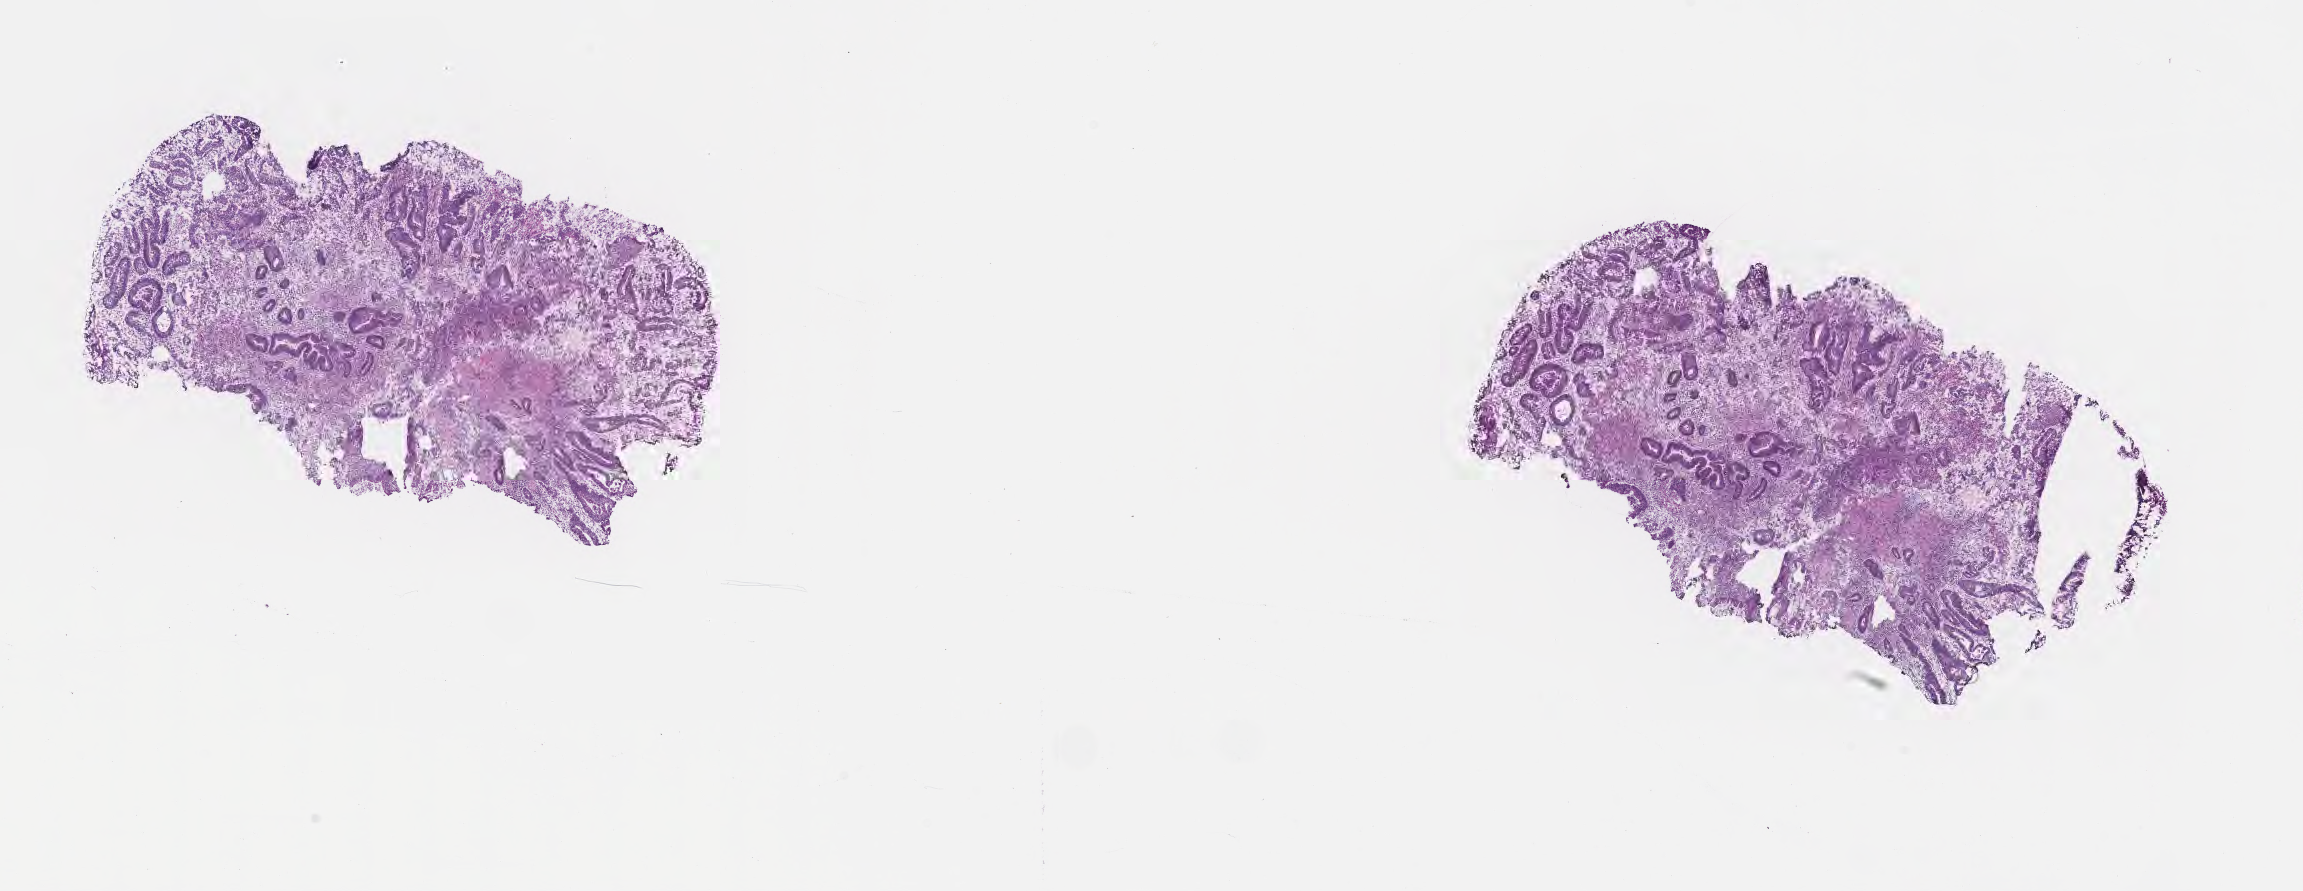
Digitized H&E-stained section, whole scanned area (about 18.6 x 7.2 mm) shown as a low-resolution overview. Frozen section (tissue freezing medium). Specimen: primary tumor. Site: sigmoid colon. Patient: male, age at initial diagnosis 67 years. Tumor grade: G2 (moderately differentiated). Pathologist review of this section (percent, as recorded): tumor cells 70%, tumor nuclei 70%, stromal cells 23%, necrosis 1%, normal cells 6%. Inflammatory infiltration, as recorded: lymphocyte infiltration 6%, monocyte infiltration 3%, neutrophil infiltration 8%.
AJCC pathologic stage: Stage IIIC. Section: top of the tissue portion. Histologic diagnosis: Adenocarcinoma, NOS.